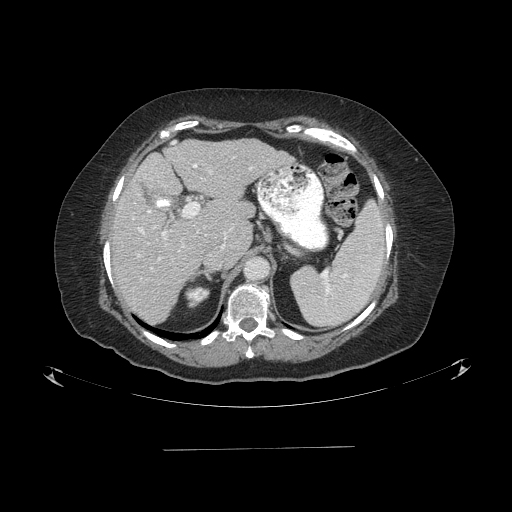
Contrast-enhanced abdominal CT (liver protocol), one axial slice; position 56 of 103 along the scan axis; one of 2 acquisitions stored at this slice position; soft-tissue window (W 400 / L 40 HU); 2.5 mm slice thickness; 512 × 512 image matrix. Case-level facts recorded for this patient, not image findings: diagnosis: hepatocellular carcinoma (patient treated with transarterial chemoembolisation; whether this scan precedes or follows treatment is not stated here); TNM stage (as recorded): Stage-IIIA.
Annotated regions visible in this slice (semi-automatic segmentation, software-assisted and operator-edited):
- liver parenchyma outside the tumour (the mass and vessels are separate outlines, so this box may not span the whole liver): bounding box (x1, y1, x2, y2) in pixels: (110, 138, 286, 324)
- liver vessels: (137, 141, 252, 269)